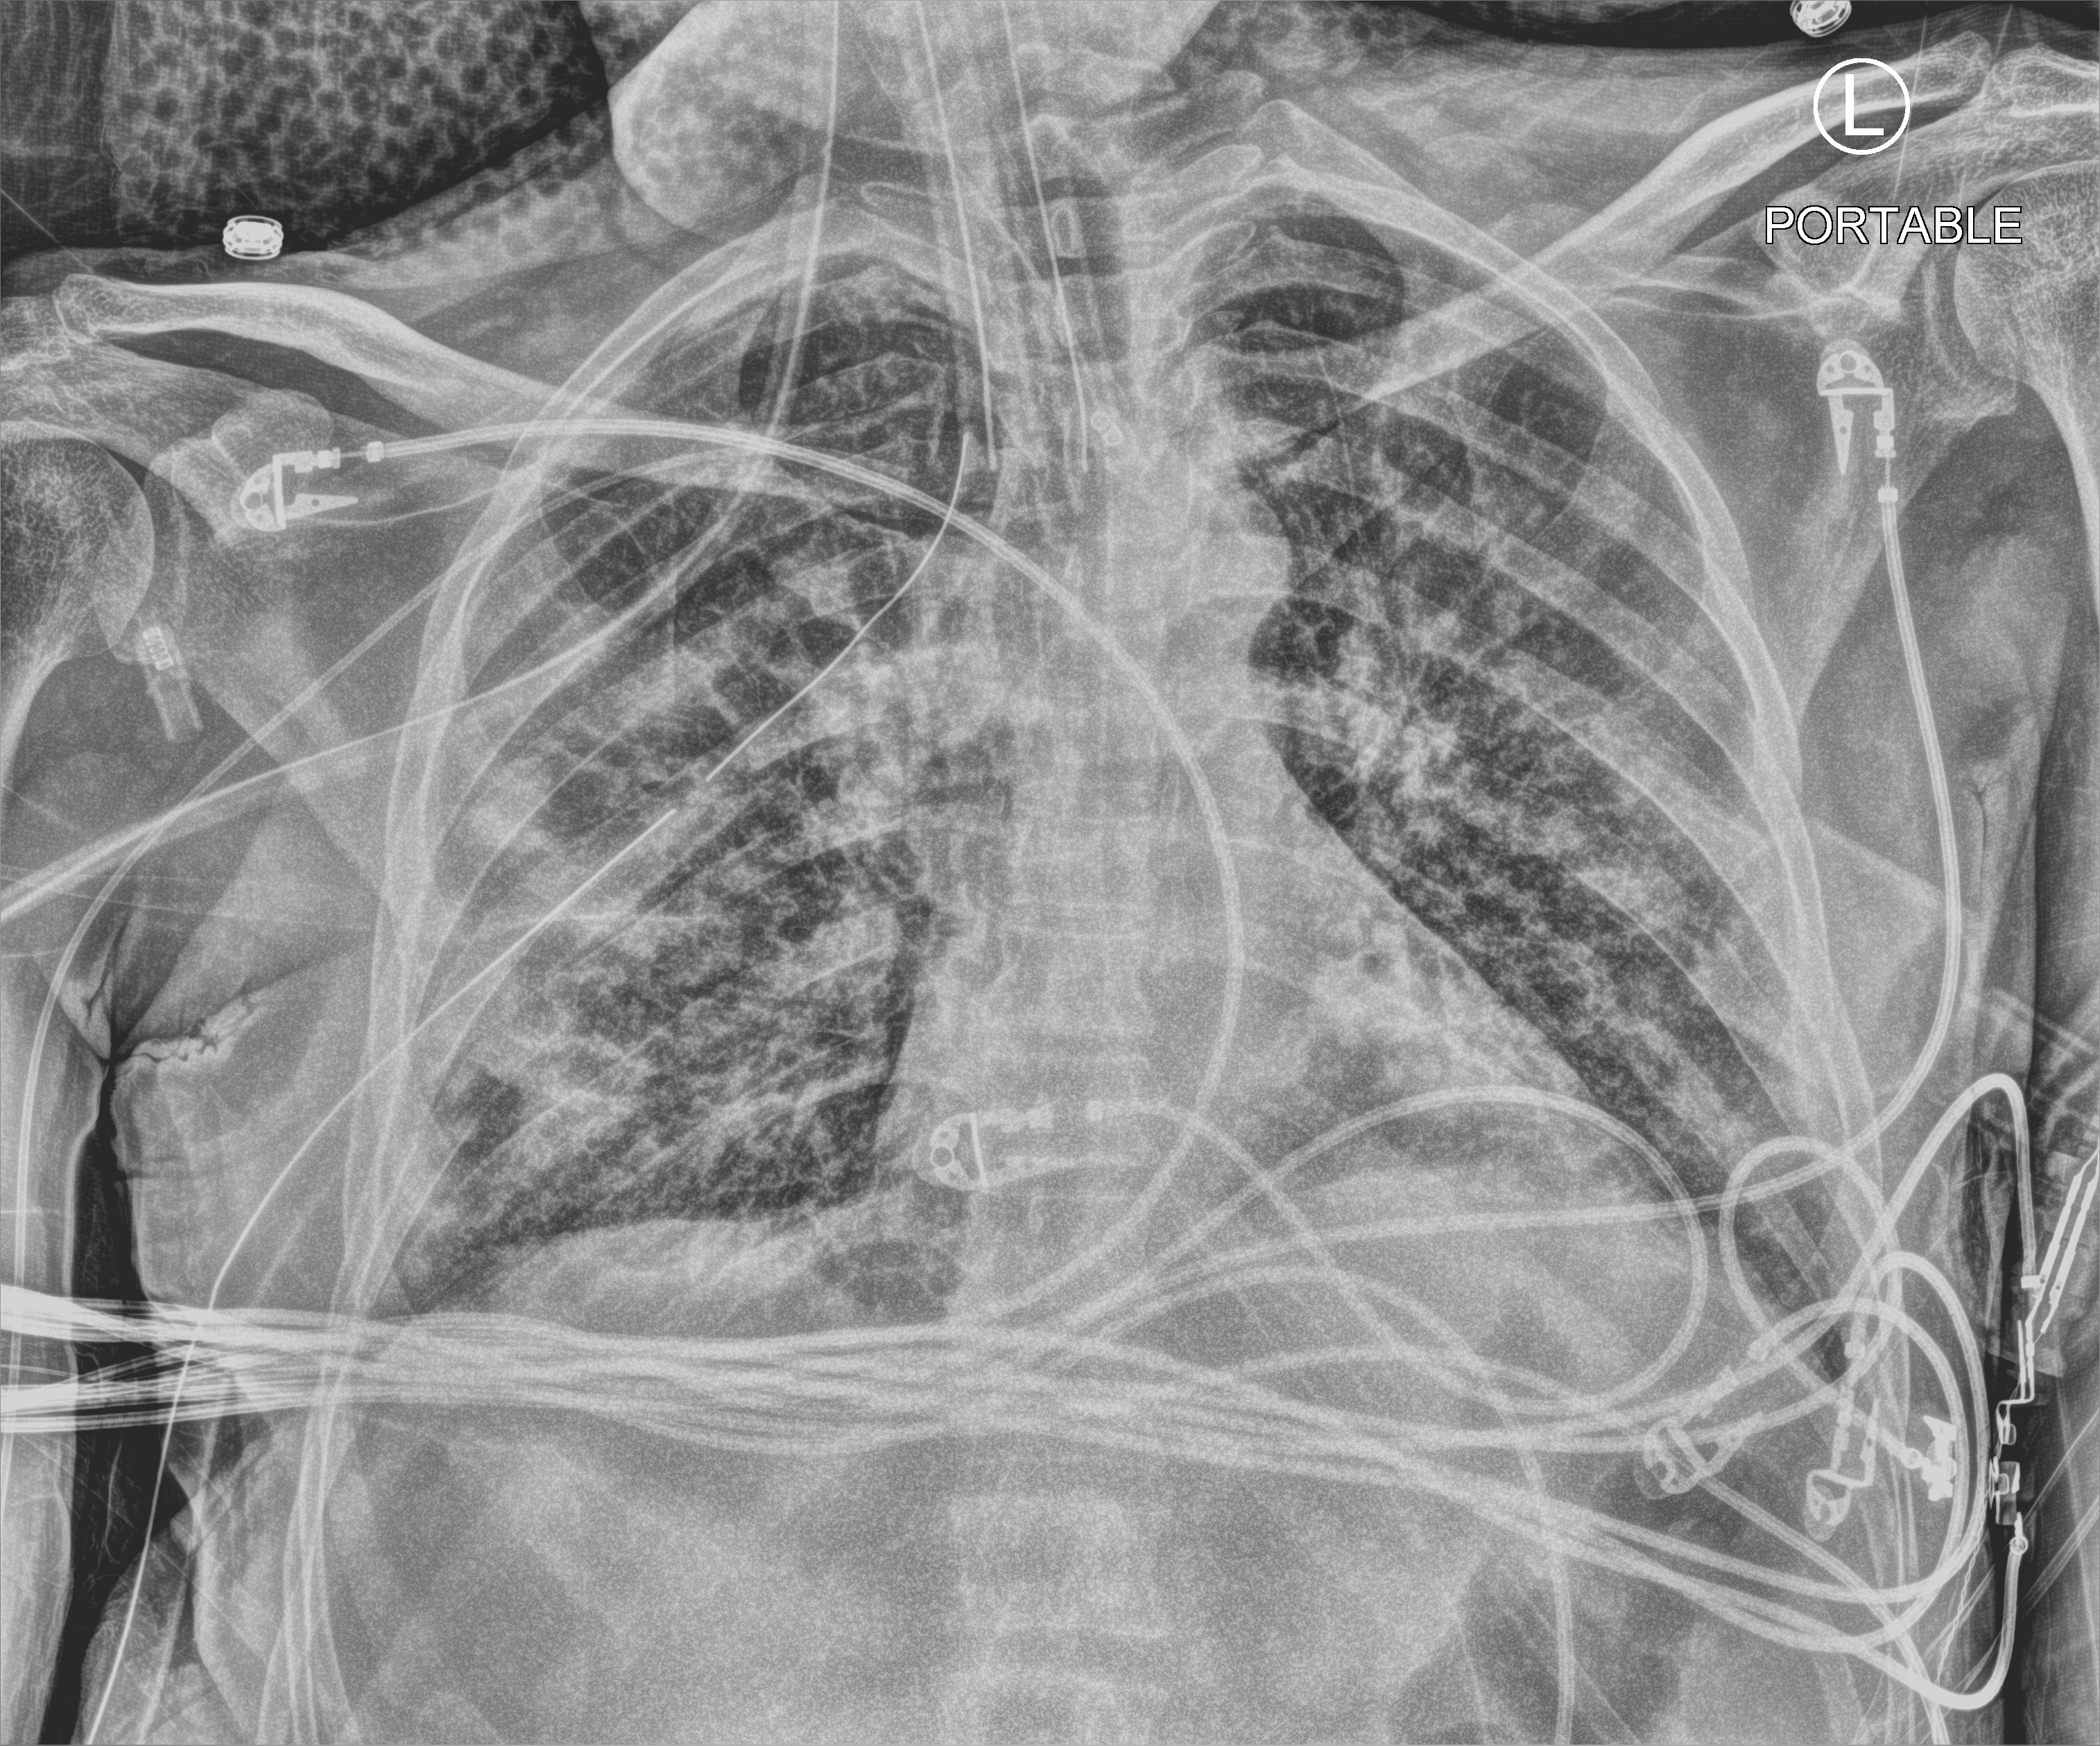
Portable chest radiograph. Male patient hospitalised with COVID-19, age 18–59 years.
Admission-level facts for this patient (not findings on this image; timing relative to this image not recorded): mechanically ventilated during this hospital stay: yes.